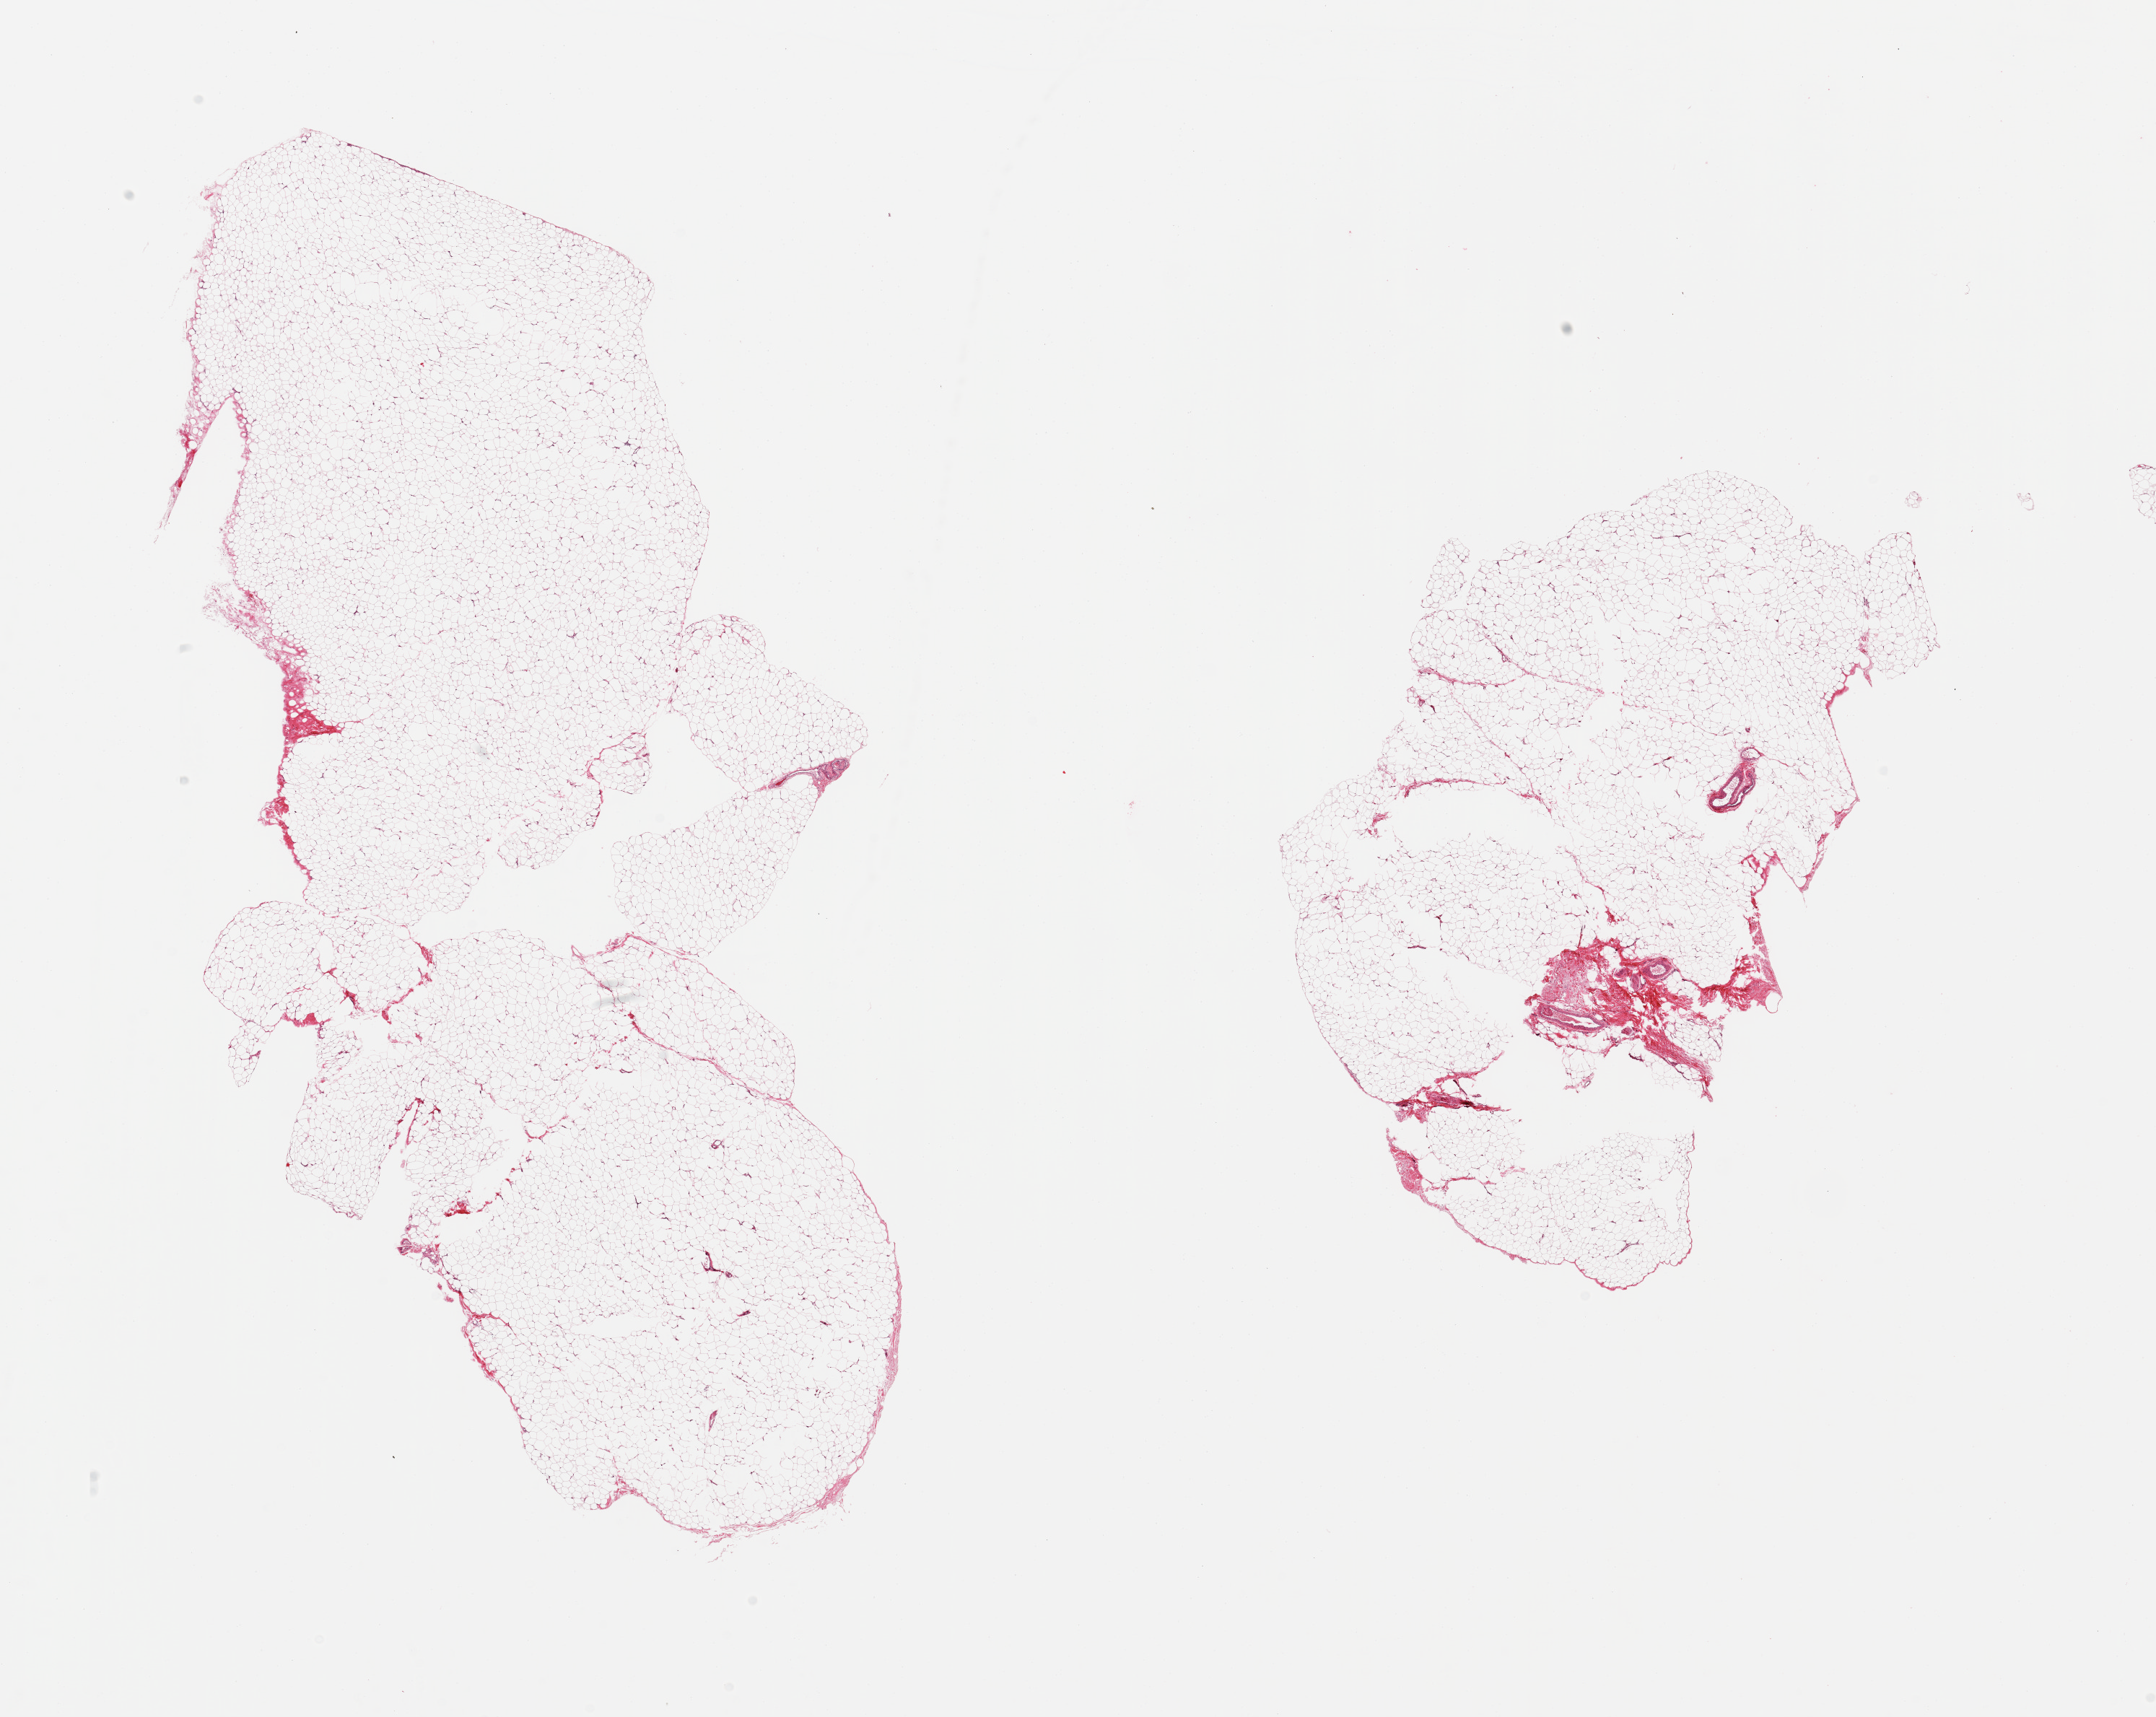
H&E whole-slide image, brightfield — a low-resolution overview of the entire scanned area, about 23.6 x 18.8 mm (slide scanned at 20x), PAXgene-fixed, paraffin-embedded tissue, sampled site (target tissue): adipose tissue, tissue donor sample. Donor: female.
Review note (as recorded): 2 pieces~5% fibrofascial tissue.